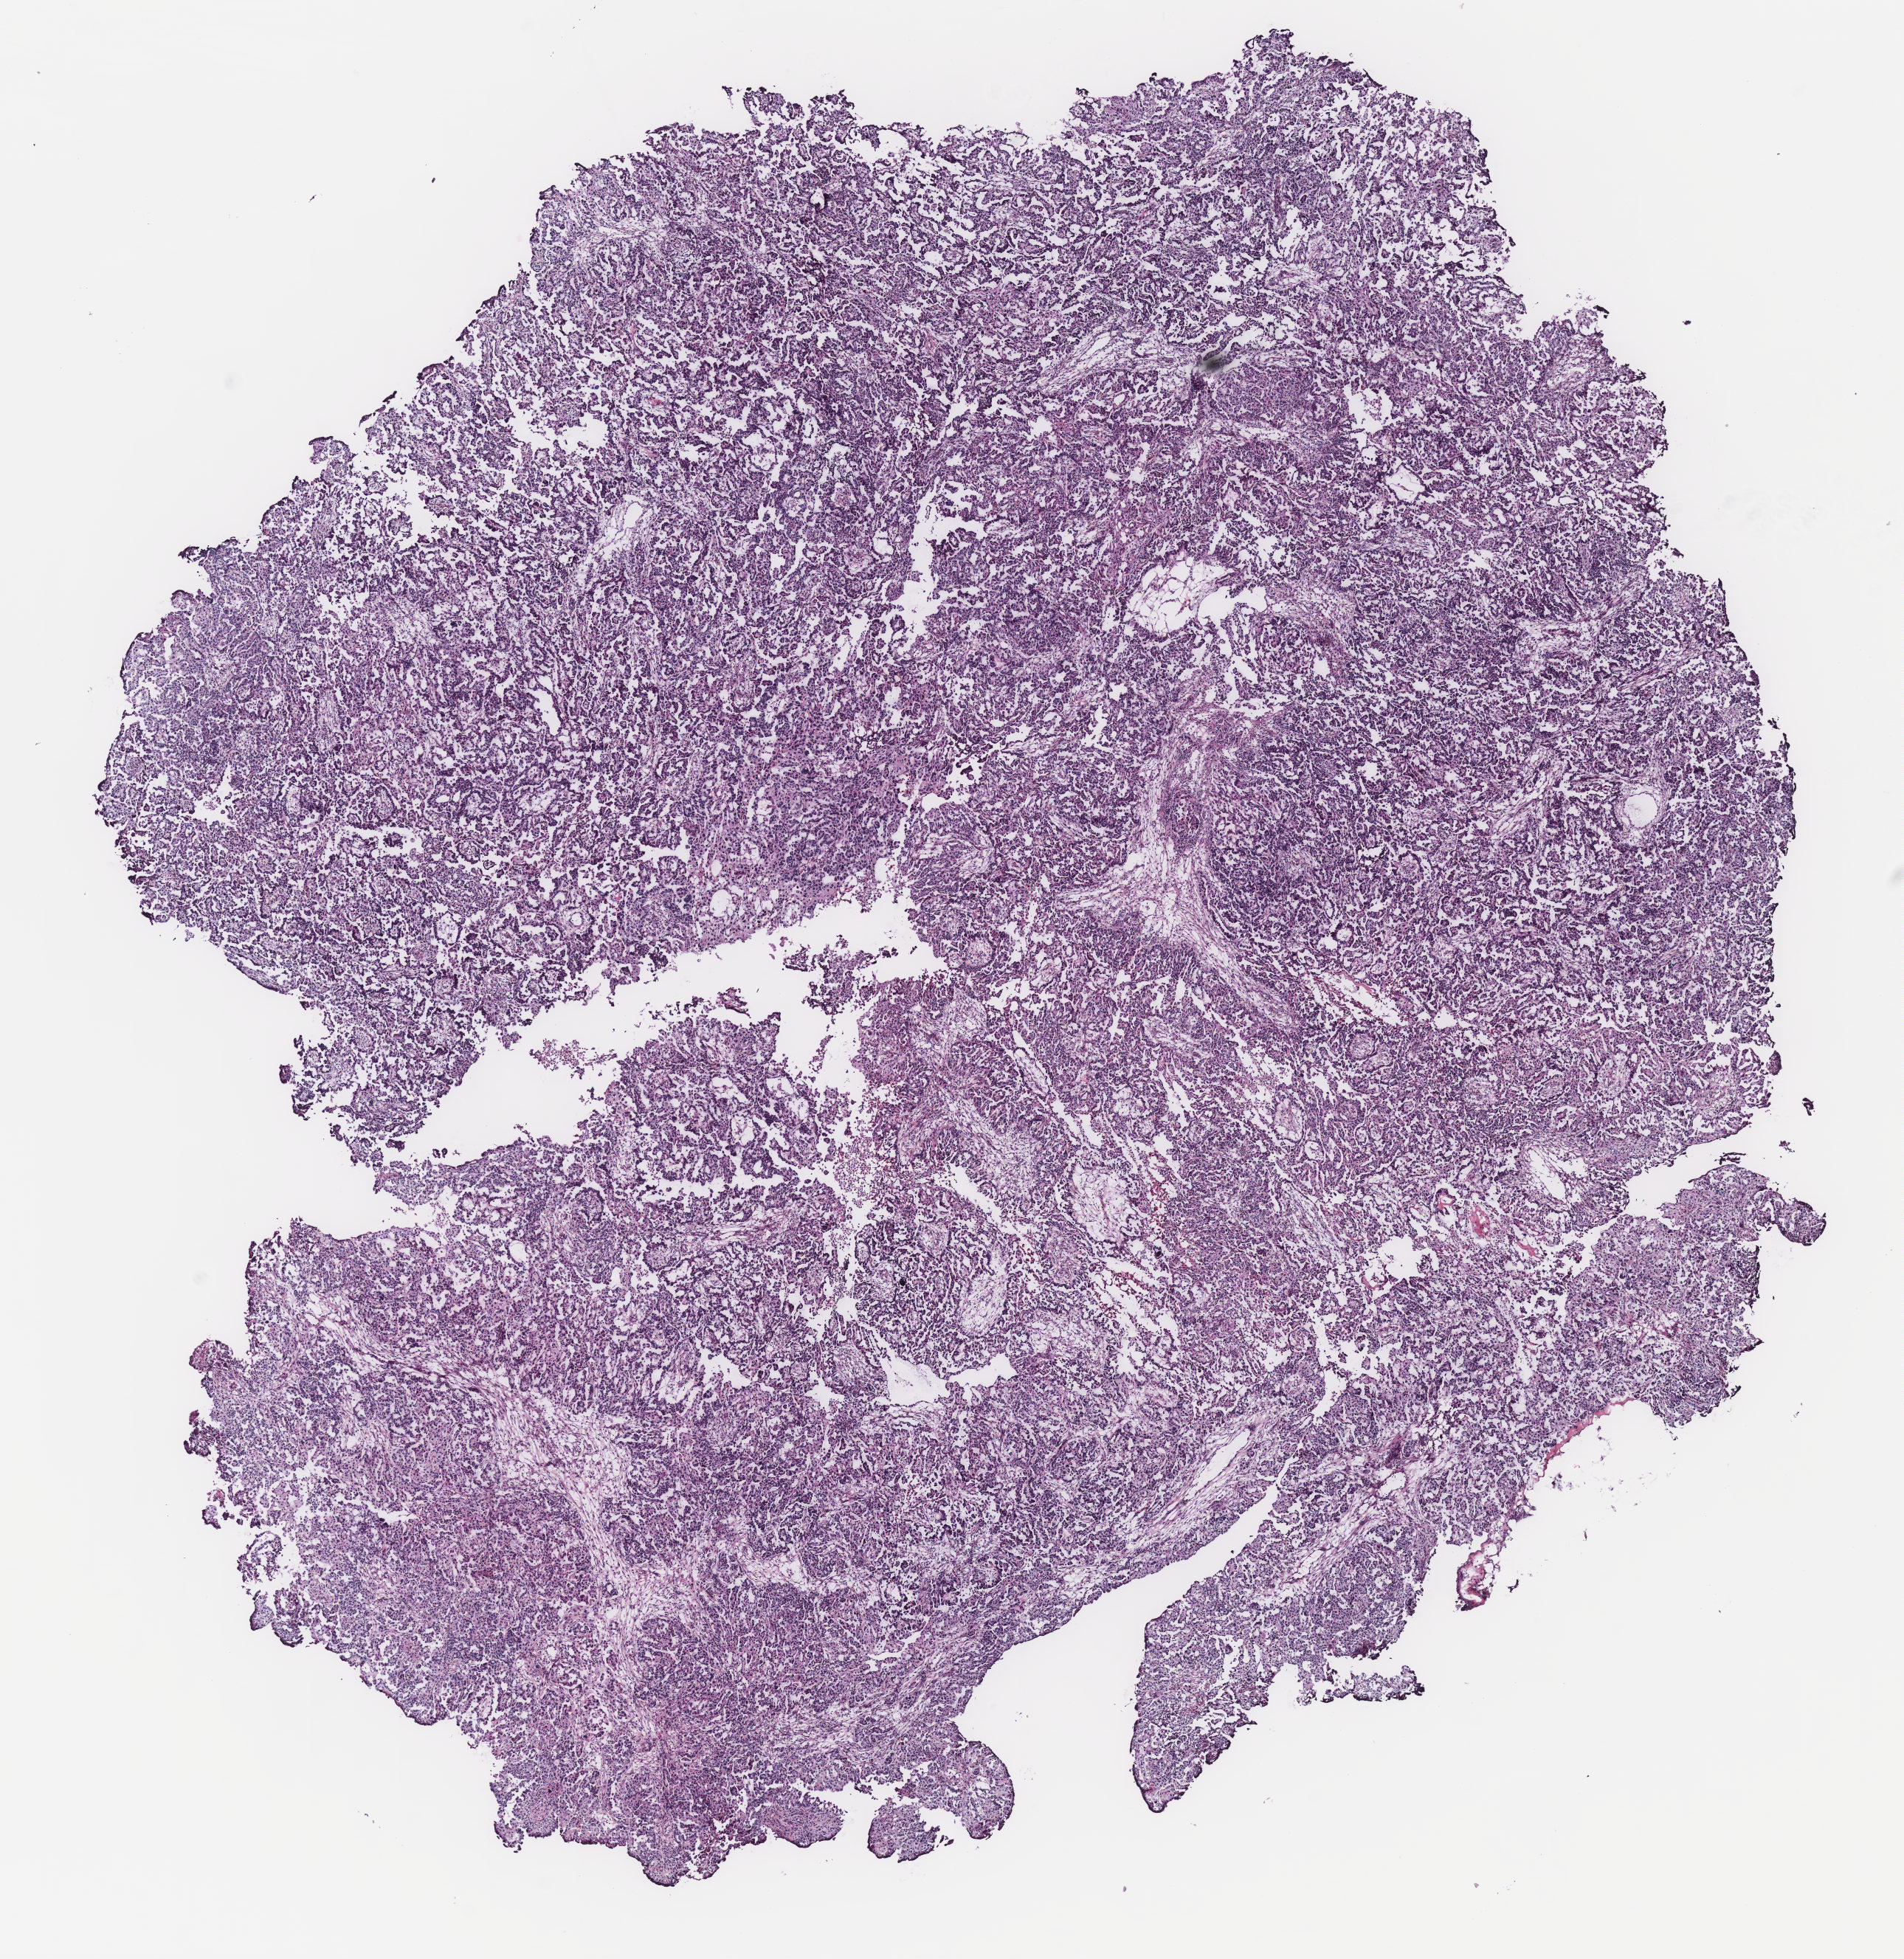
H&E whole-slide image — shown as a low-resolution overview of the whole scanned area (about 10.3 x 10.6 mm). Ovary, tissue type not recorded. Female patient.
Patient diagnosis: Serous adenocarcinoma, NOS.